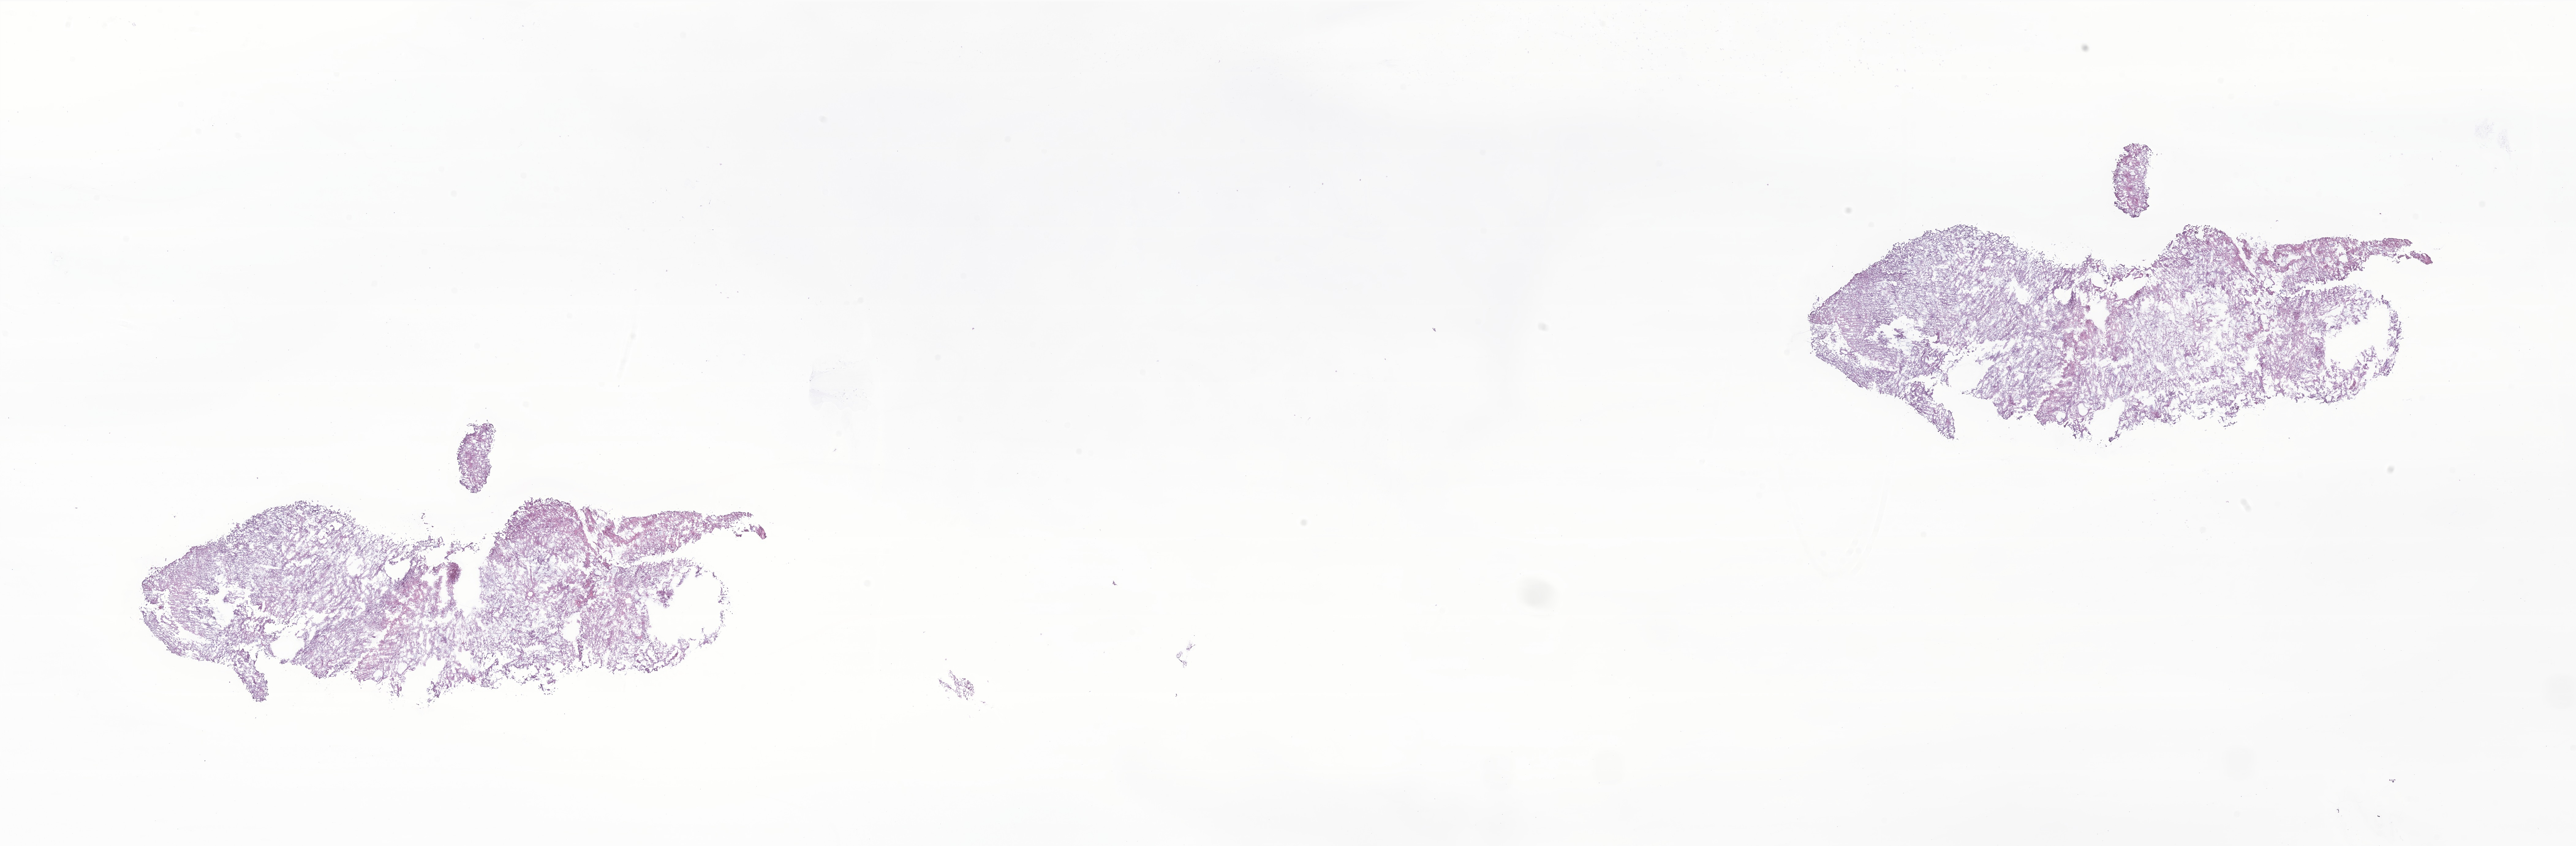
Digitized haematoxylin and eosin-stained section of tumor tissue from the spinal cord, shown as a low-resolution overview of the whole scanned area (about 35.5 x 11.6 mm). Frozen section. Patient female; age 166 months (13 years 10 months).
Recorded diagnosis: Myxopapillary ependymoma.